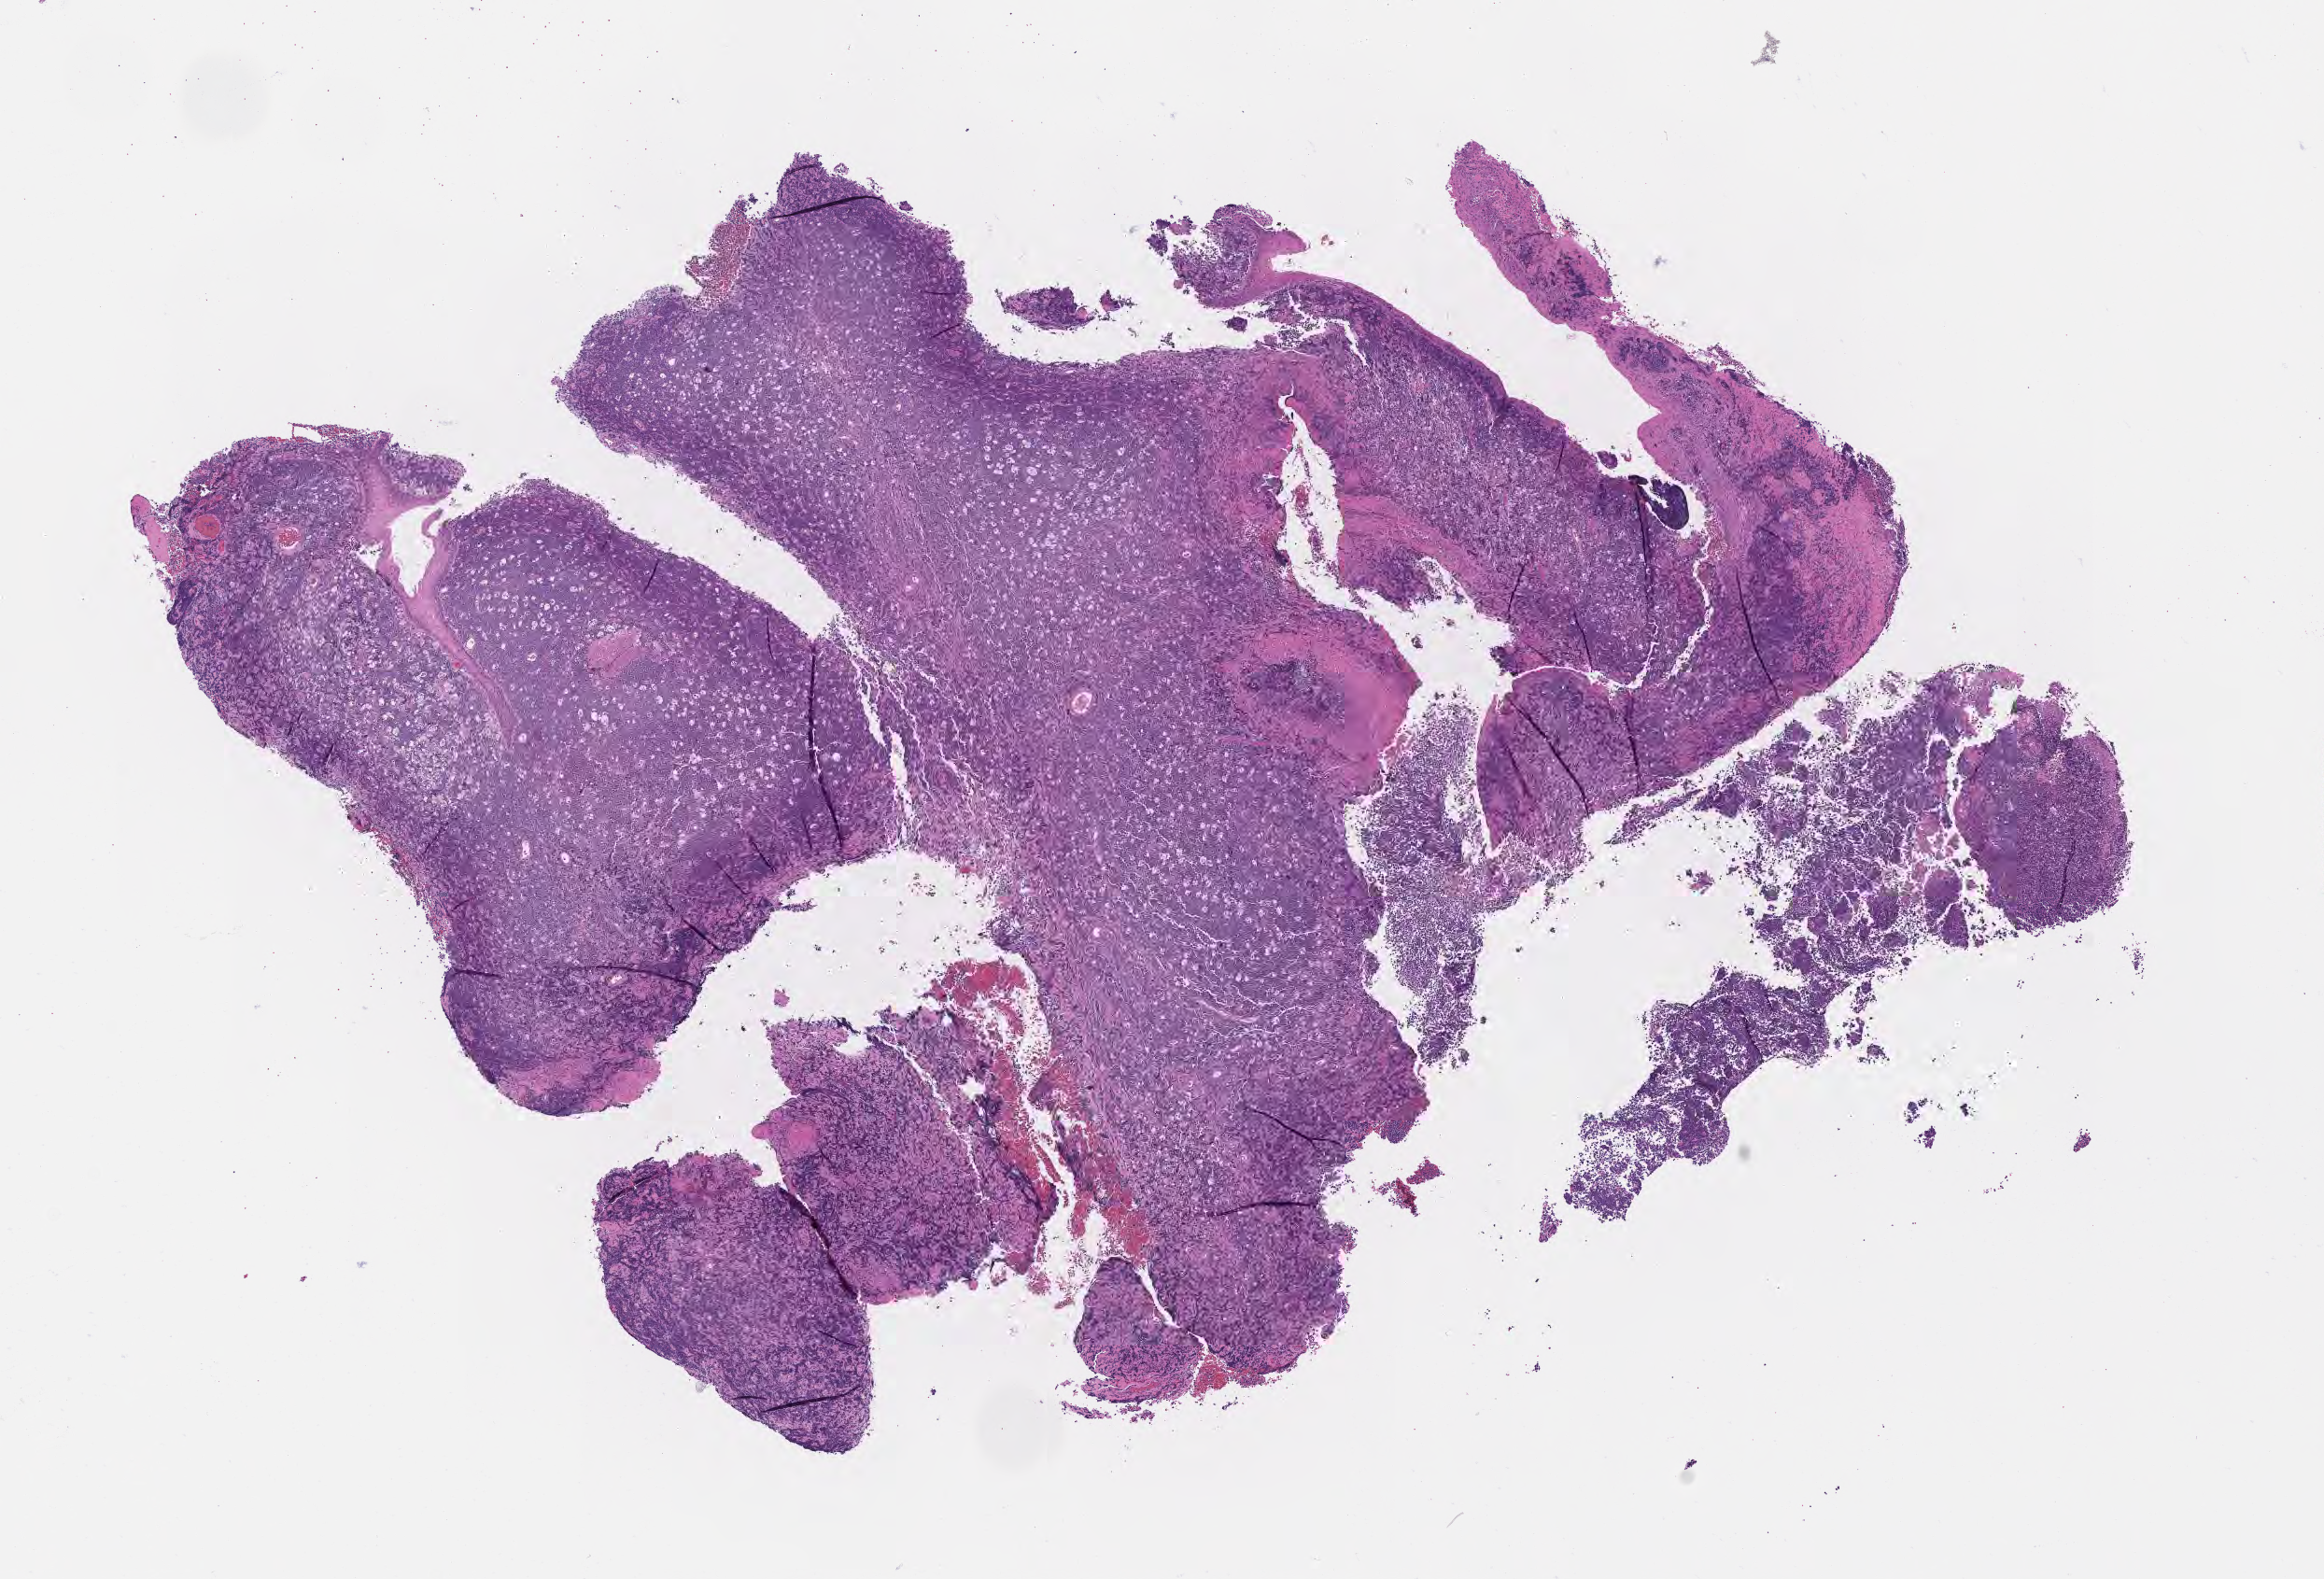
H&E whole-slide image — low-resolution overview of the scanned area, about 10.1 x 6.8 mm. Tumor tissue. Patient: male, age at initial diagnosis 3 years.
Diagnosis: Burkitt lymphoma, NOS.